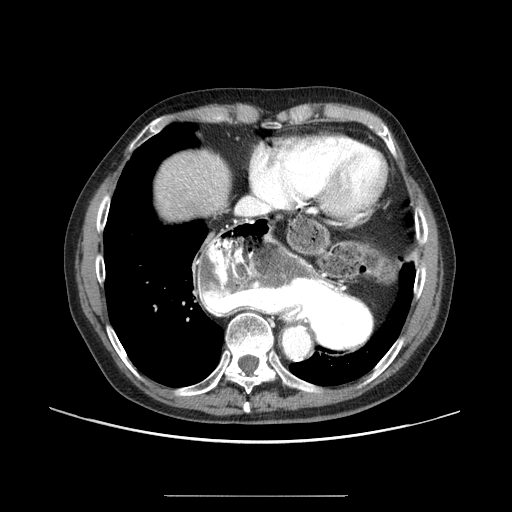
Contrast-enhanced abdominal CT (liver protocol), one axial slice. Slice 79 of 91 in the series (ordered by position). 100 kVp. One of 2 acquisitions stored at this slice position. Soft-tissue window (W 400 / L 40 HU). 2.5 mm slice thickness. 512 × 512 image matrix, field of view 400 × 400 mm. Case-level facts recorded for this patient, not image findings: diagnosis: hepatocellular carcinoma (patient treated with transarterial chemoembolisation; whether this scan precedes or follows treatment is not stated here); TNM stage (as recorded): Stage-I; Child-Pugh class: A; tumour differentiation: moderately differentiated; tumour nodularity: uninodular.
Outlined on this slice (semi-automatic segmentation, software-assisted and operator-edited):
- abdominal aorta: box from (x=284, y=327) to (x=309, y=358) px
- liver parenchyma outside the tumour (the mass and vessels are separate outlines, so this box may not span the whole liver): (x=154, y=152)–(x=230, y=220)